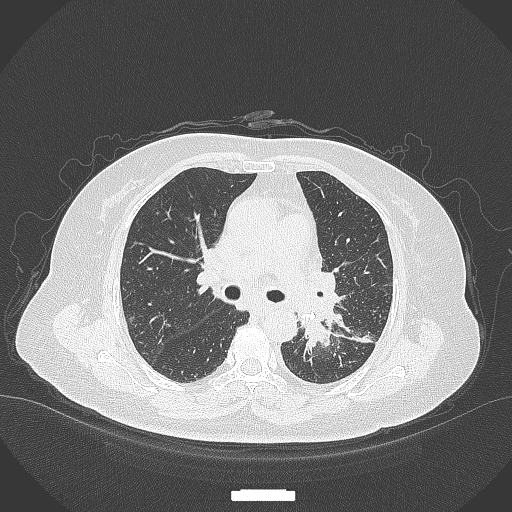
Chest CT, one axial slice. 120 kVp. Lung window (W 1500 / L -600 HU). 1 mm slice thickness. 512 × 512 image matrix, field of view 400 × 400 mm. Female patient, age 69 years. Case-level facts recorded for this patient, not image findings: clinical TNM (as recorded): T2b N3 M1.
Annotated regions visible in this slice (bounding box drawn by a radiologist):
- lung tumour (recorded histology: adenocarcinoma): box from (x=294, y=314) to (x=335, y=361) px